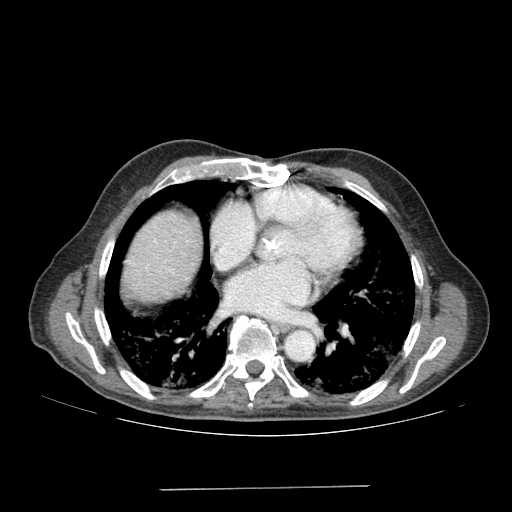
Contrast-enhanced abdominal CT (liver protocol), one axial slice; position 176 of 192 along the scan axis; 120 kVp; soft-tissue window (W 400 / L 40 HU); 2.5 mm slice thickness; 512 × 512 image matrix. Case-level facts recorded for this patient, not image findings: diagnosis: hepatocellular carcinoma (patient treated with transarterial chemoembolisation; whether this scan precedes or follows treatment is not stated here); TNM stage (as recorded): Stage-IVA; Child-Pugh class: A; tumour differentiation: poorly differentiated; tumour nodularity: uninodular.
Structures marked on this image (semi-automatic segmentation, software-assisted and operator-edited):
- liver parenchyma outside the tumour (the mass and vessels are separate outlines, so this box may not span the whole liver): box from (x=123, y=212) to (x=200, y=302) px